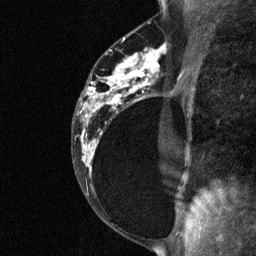
Breast MRI (dynamic contrast-enhanced), one sagittal slice; slice 39 of 64 in the series (ordered by position); dynamic contrast-enhanced study with each time point stored as its own series, time point 2 of 3 at this slice position (early post-contrast, ordered by acquisition time); 1.5 T; TE 4.8 ms, TR 27 ms; 2 mm slice thickness; 256 × 256 image matrix. Female patient, age 34 years. From the clinical record (not read from this slice): setting: breast cancer imaged before/during neoadjuvant chemotherapy; receptor status: HR-positive, HER2-negative.
Outlined on this slice (semi-automatically segmented with operator editing):
- analysis volume of interest (the breast-tissue region the enhancement analysis was run in; not a lesion): bounding box [x1, y1, x2, y2] px = [78, 44, 181, 191]
- tumour enhancement mask (voxels above the 90 % enhancement threshold inside the analysis volume of interest): [82, 48, 165, 168]